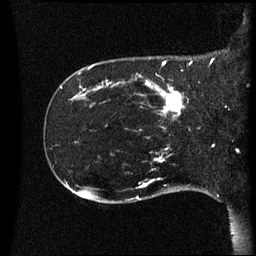
Breast MRI (dynamic contrast-enhanced), one sagittal slice. Position 12 of 60 along the scan axis. Dynamic contrast-enhanced series, image 2 of 3 at this slice position (ordered by acquisition). 1.5 T. TE 4.2 ms, TR 8.4 ms. 2.2 mm slice thickness. 256 × 256 image matrix, field of view 220 × 220 mm. Patient: female, 41 years. From the clinical record (not read from this slice): setting: breast cancer imaged before/during neoadjuvant chemotherapy; receptor status: HER2-positive.
Structures marked on this image (semi-automatic segmentation, software-assisted and operator-edited):
- analysis volume of interest (the breast-tissue region the enhancement analysis was run in; not a lesion): bounding box (x1, y1, x2, y2) in pixels: (122, 80, 197, 121)
- tumour enhancement mask (voxels above the 70 % enhancement threshold inside the analysis volume of interest): (146, 80, 186, 117)